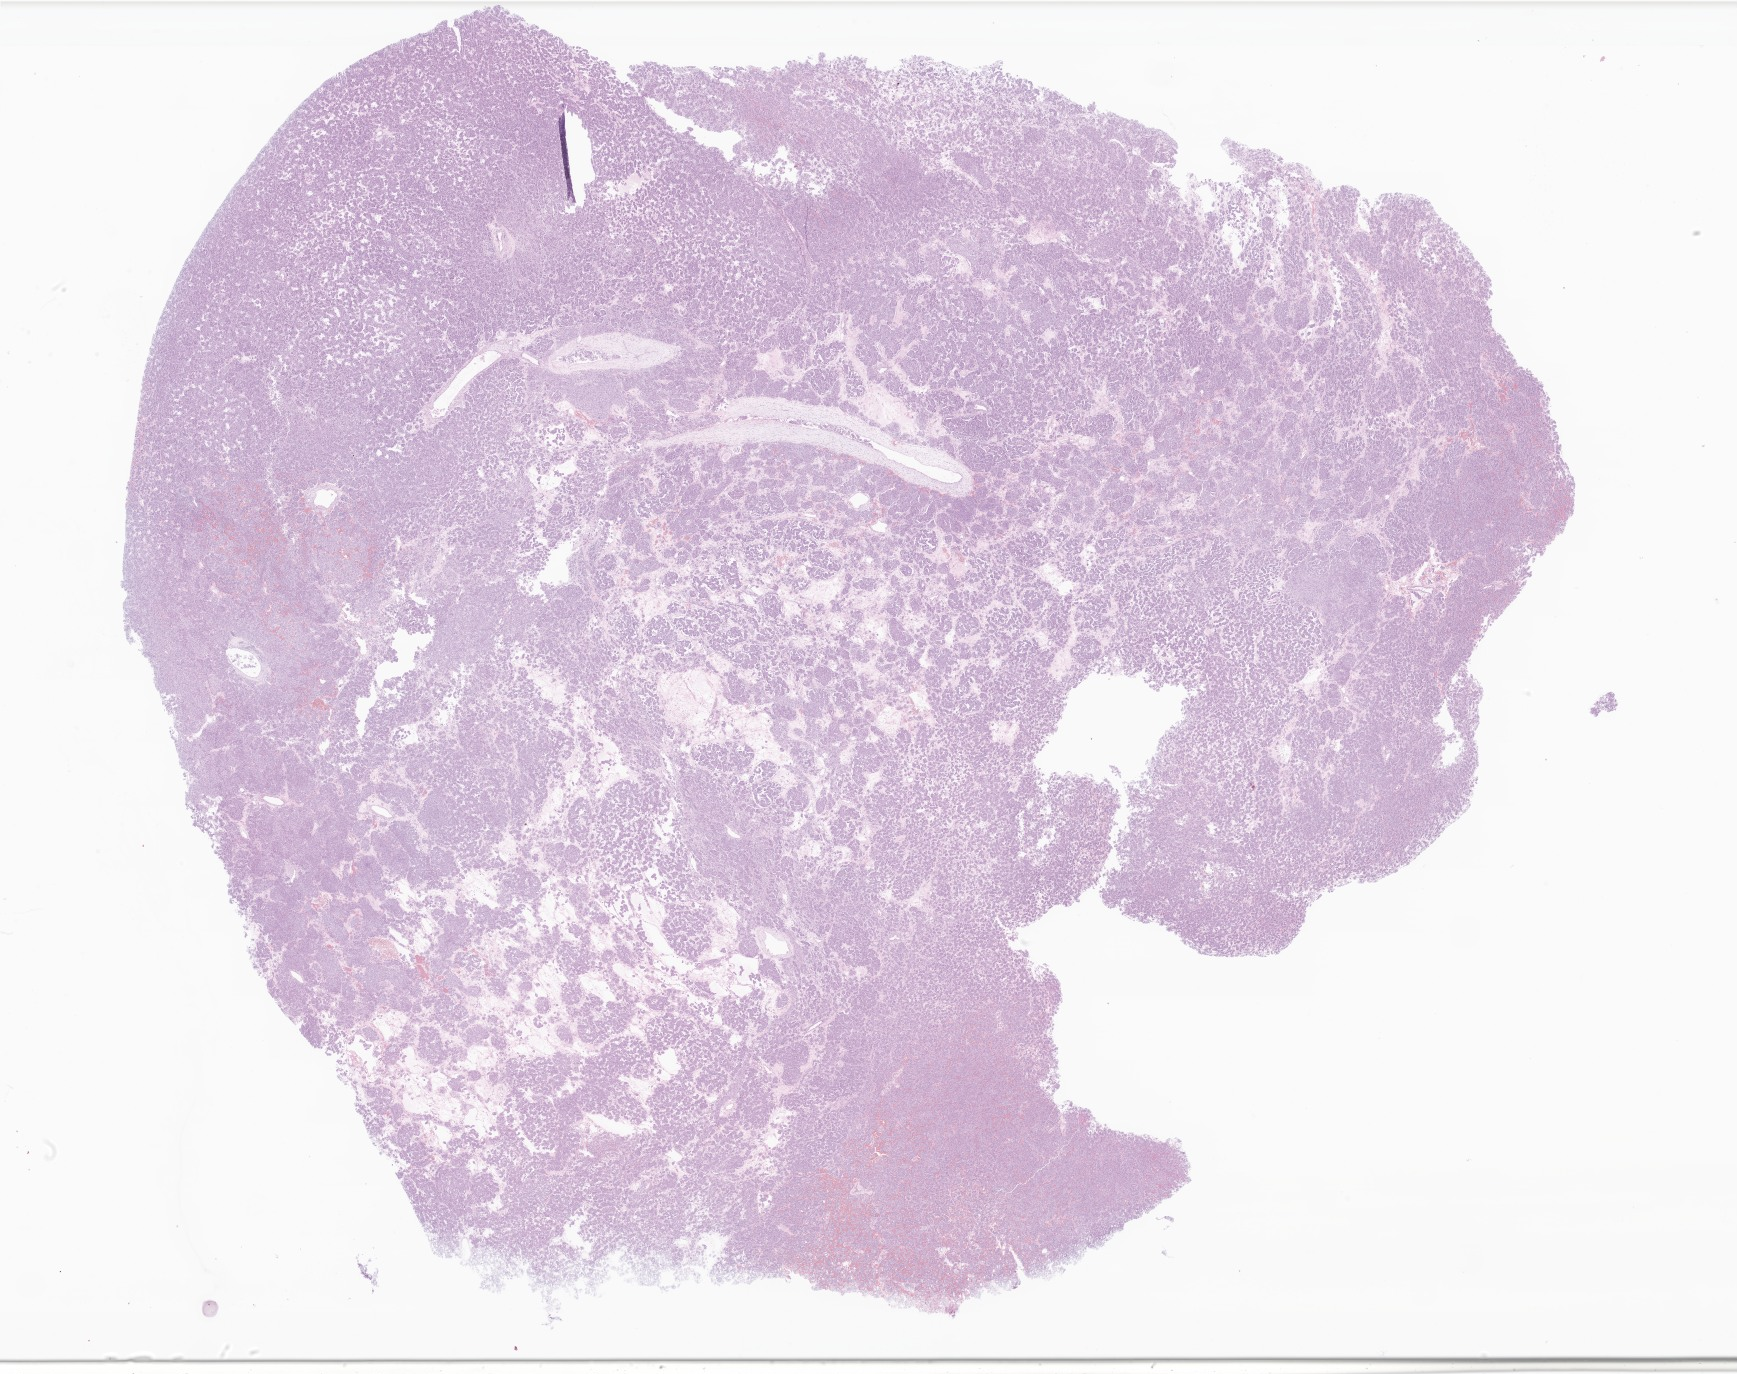
Digitized haematoxylin and eosin-stained section of tumor tissue from the stomach, whole scanned area (about 29.3 x 23.2 mm) shown as a low-resolution overview. Female patient, age 201 months.
Specimen: formalin-fixed paraffin-embedded section.